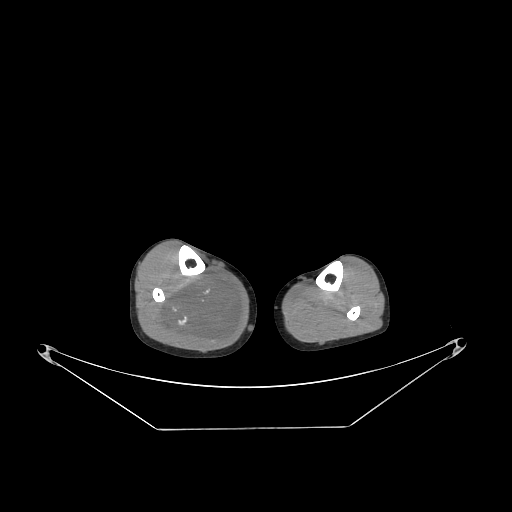
CT of an extremity soft-tissue mass (from a PET/CT study), one axial slice; slice 103 of 267 in the series (ordered by position); reconstruction kernel STANDARD; soft-tissue window (W 400 / L 40 HU); 512 × 512 image matrix, field of view 500 × 500 mm. Male patient. From the clinical record (not read from this slice): histological type: liposarcoma - round cell; grade: high; site of the primary tumour: right calf.
Annotated regions visible in this slice (expert contour drawn on MRI and transferred to this co-registered scan by the dataset authors):
- gross tumour volume (mass): bounding box <155,272,241,346> (left, top, right, bottom; pixels)